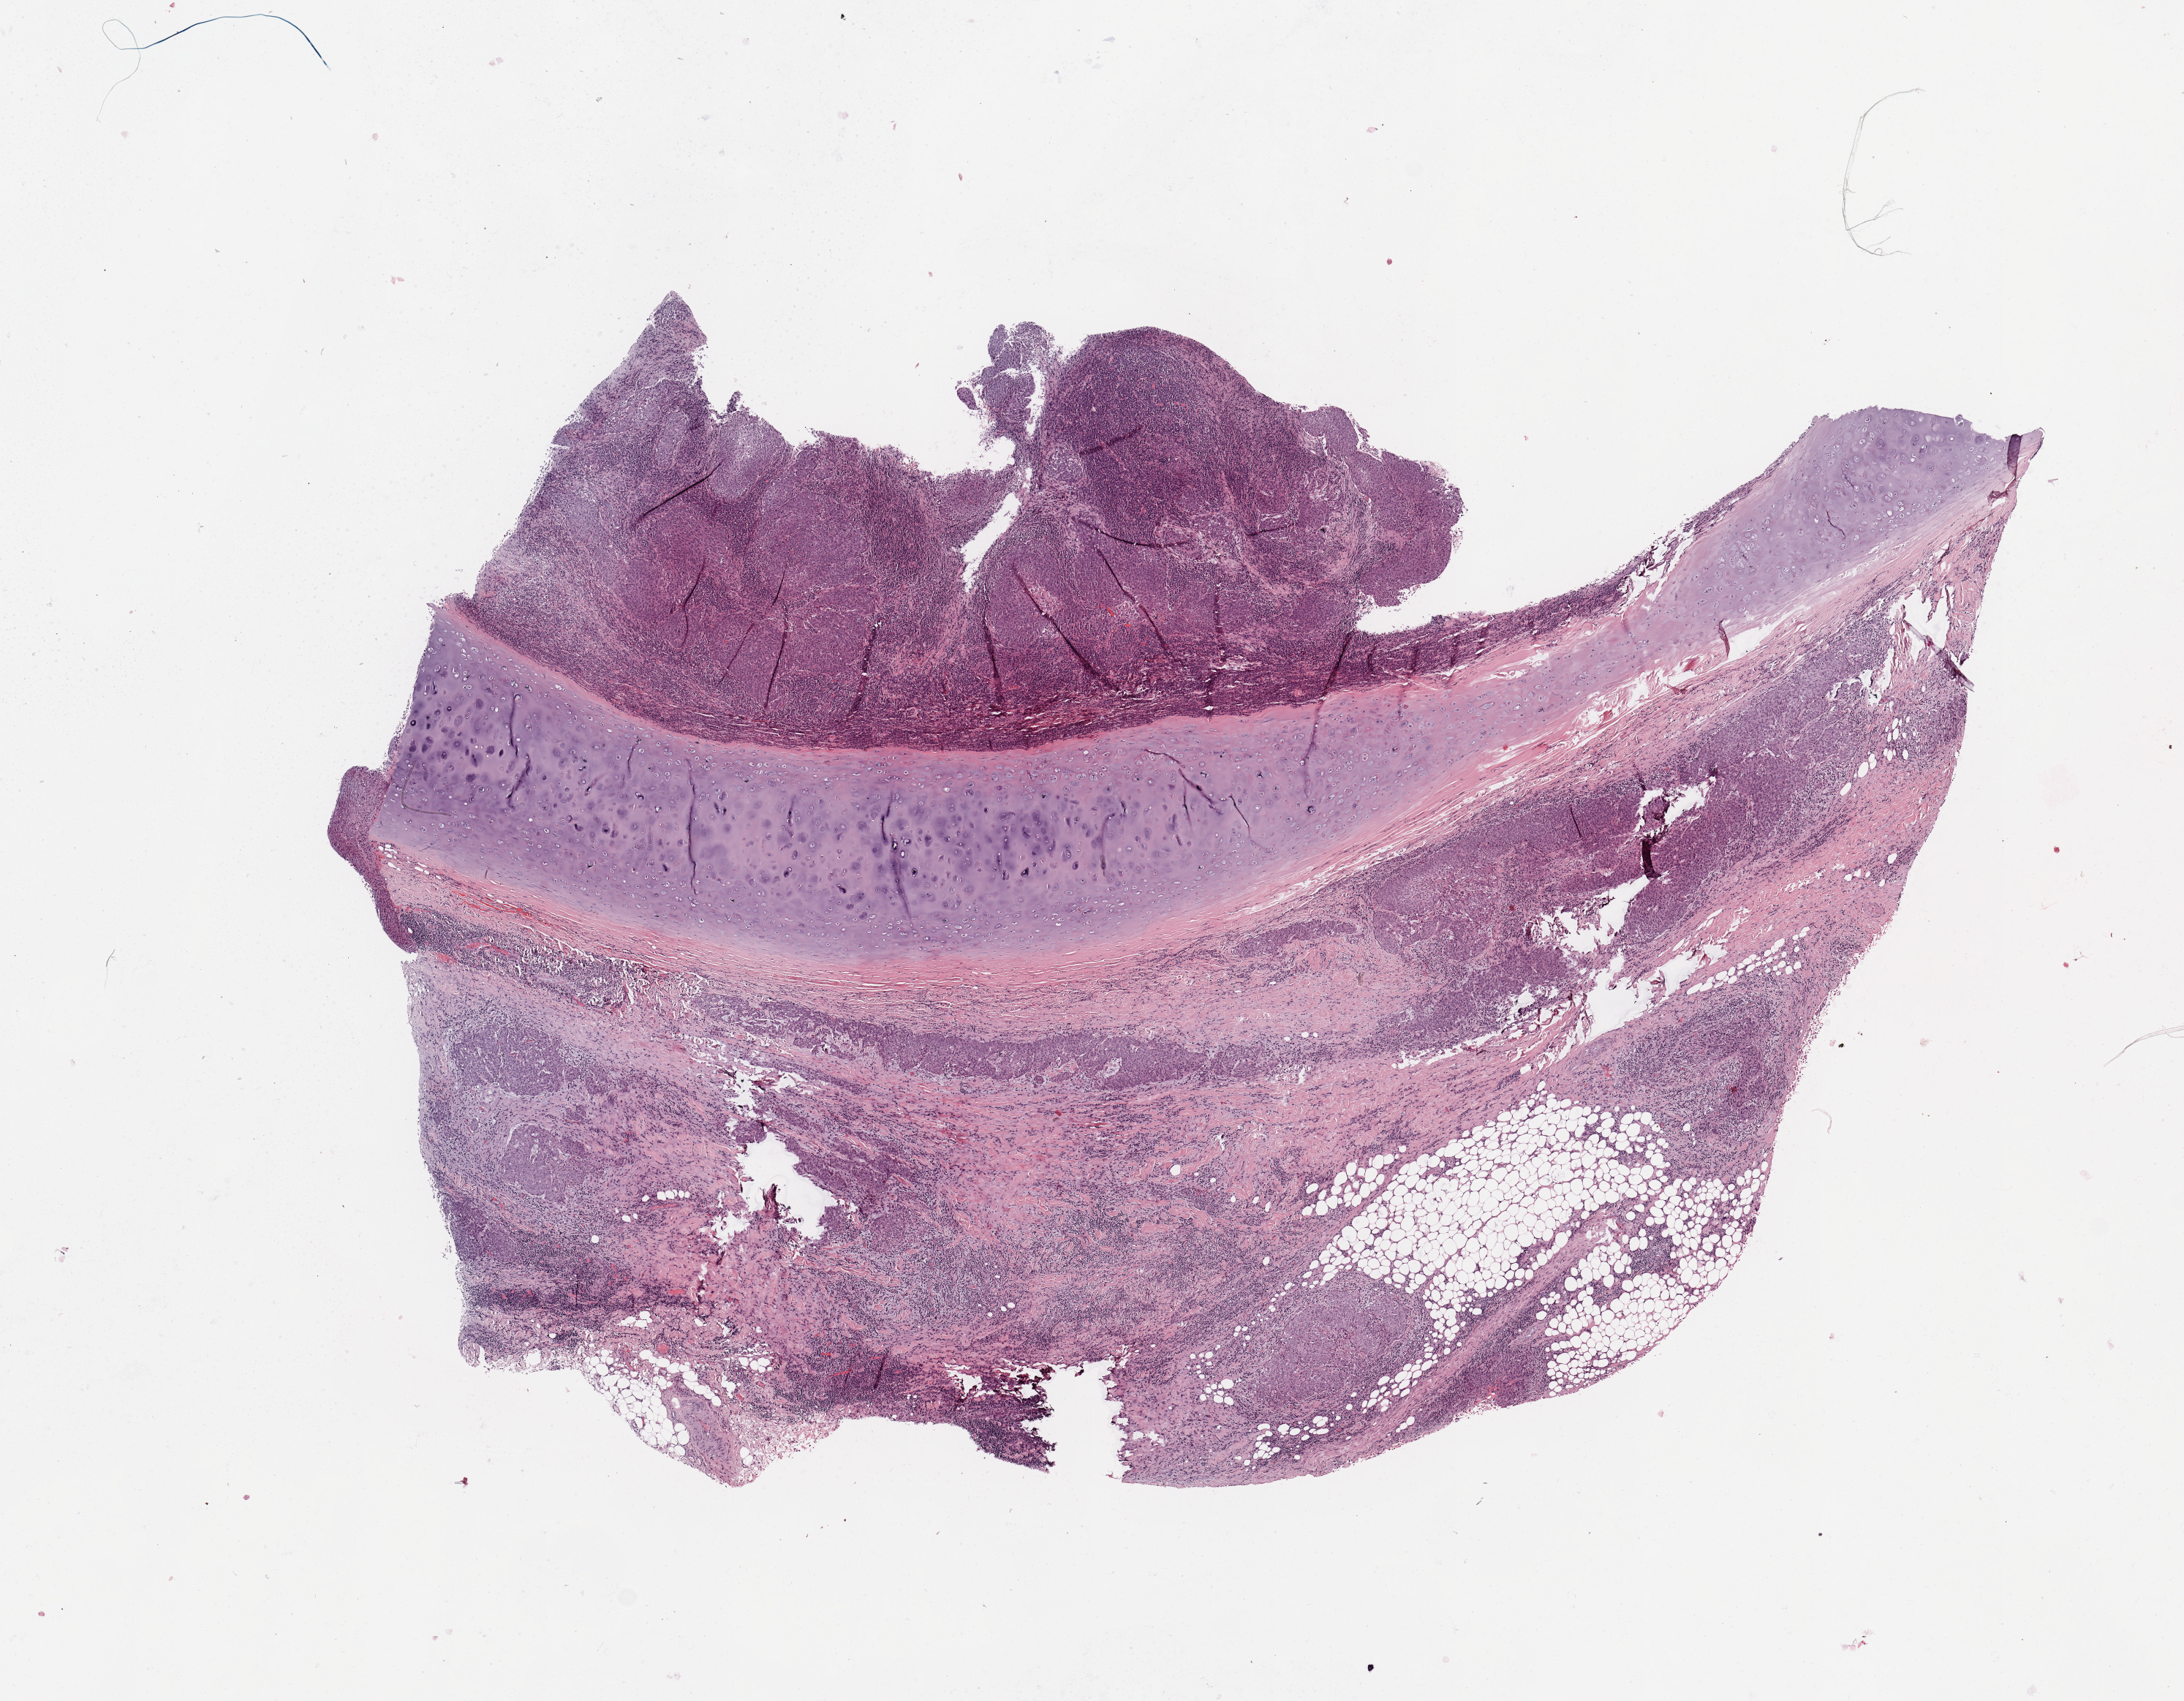
Hematoxylin and eosin (H&E) stained whole-slide image — a low-resolution overview of the entire scanned area, about 11.8 x 9.2 mm (acquisition: 20x scan); lung, tumour tissue. 66-year-old male patient. Histologic grade: G3 (poorly differentiated).
* diagnosis: Squamous cell carcinoma, NOS
* AJCC pathologic stage: IIA